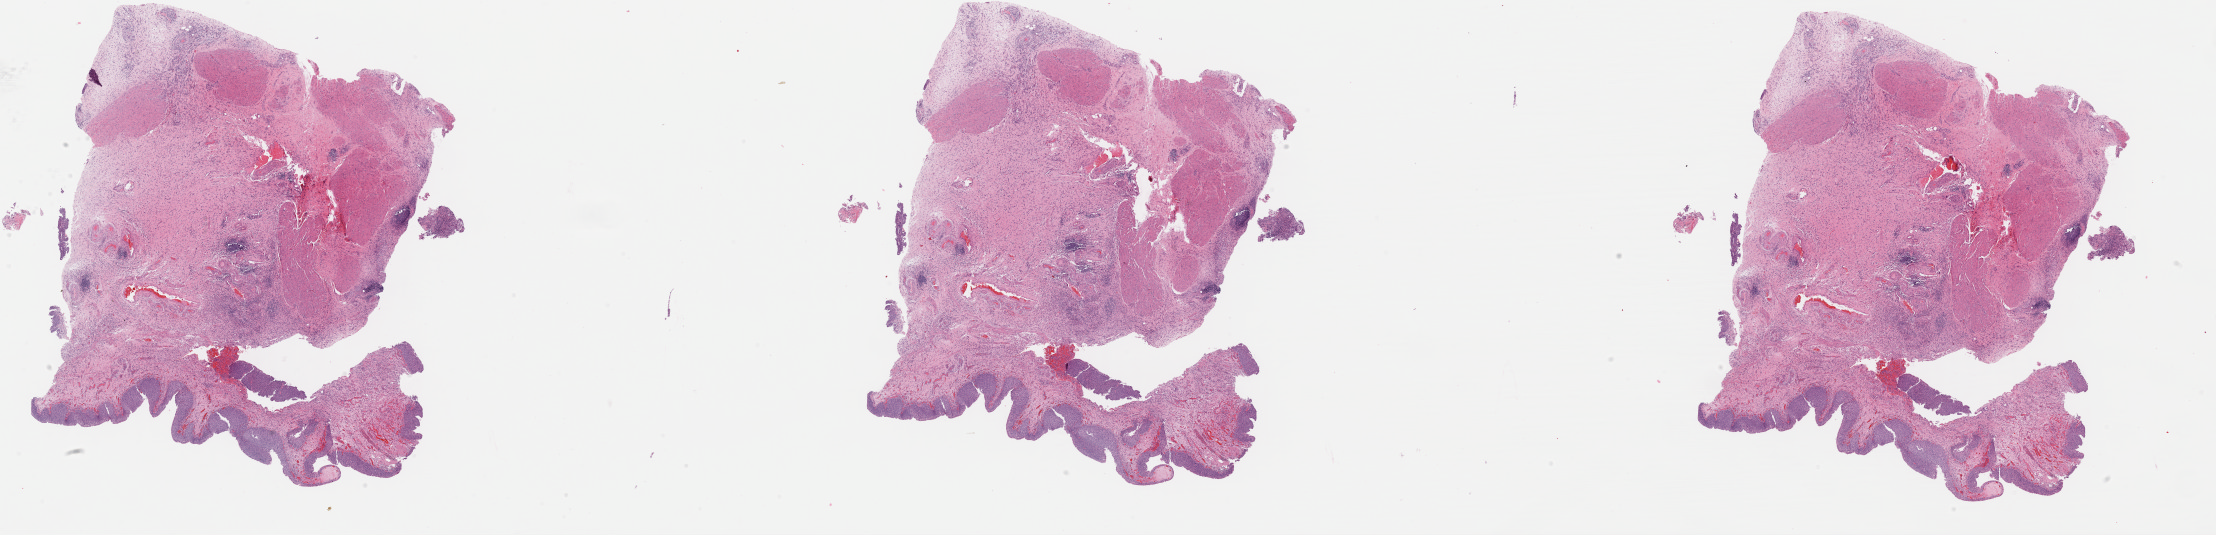
Whole-slide histology image, Hematoxylin and eosin (H&E) stained, a low-resolution overview of the entire scanned area, about 35.0 x 8.5 mm (acquisition: 40x scan), formalin-fixed paraffin-embedded (FFPE) diagnostic section, primary tumour sample from the bladder. Male, age 48 years at initial diagnosis. Histologic grade: high grade.
Lymph nodes positive (case pathology): 1 of 15 examined. Pathologic diagnosis: Transitional cell carcinoma. AJCC pathologic stage: IV (7th edition).